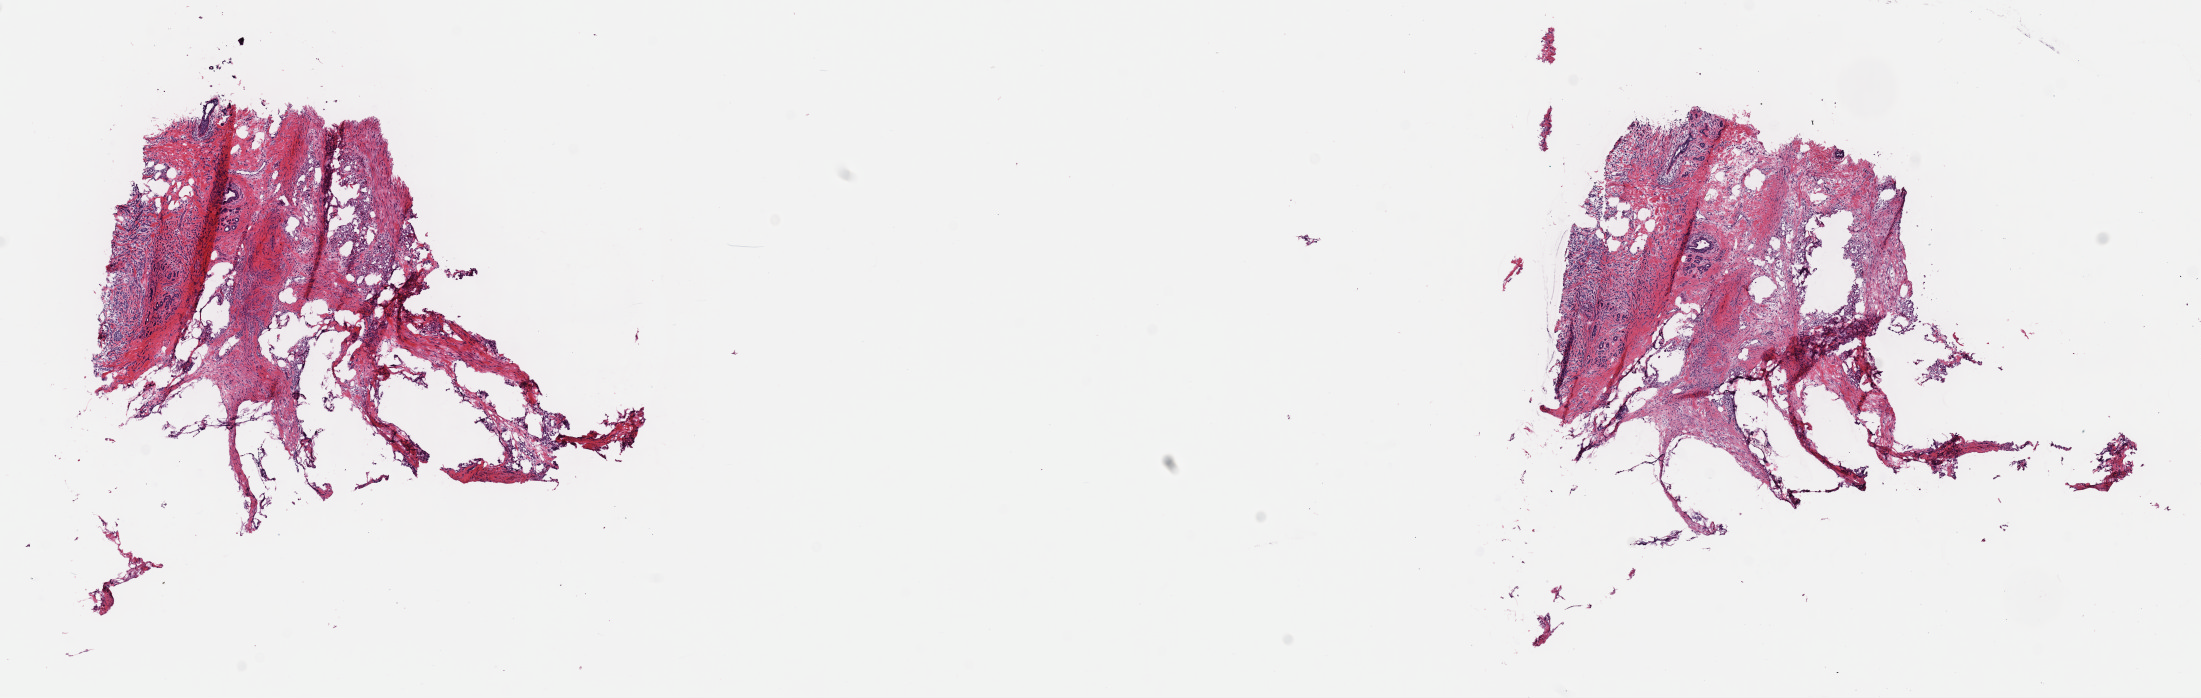
H&E-stained whole-slide image, a low-resolution overview of the entire scanned area, about 17.4 x 5.5 mm (slide scanned at 40x), frozen section from the top of the tissue portion, primary tumour sample from the breast. Female patient; age at initial diagnosis 40 years. Pathologist review of this section (percent, as recorded): tumour cells 40%, tumour nuclei 70%, normal cells 10%, stromal cells 50%, necrosis 0%. Inflammatory infiltration, as recorded: lymphocyte infiltration 1%, monocyte infiltration 0%, neutrophil infiltration 0%.
Diagnosis: Lobular carcinoma, NOS. Lymph nodes positive (case pathology): 1 of 18 examined. Laterality: left. AJCC pathologic stage: IIIA (6th edition).